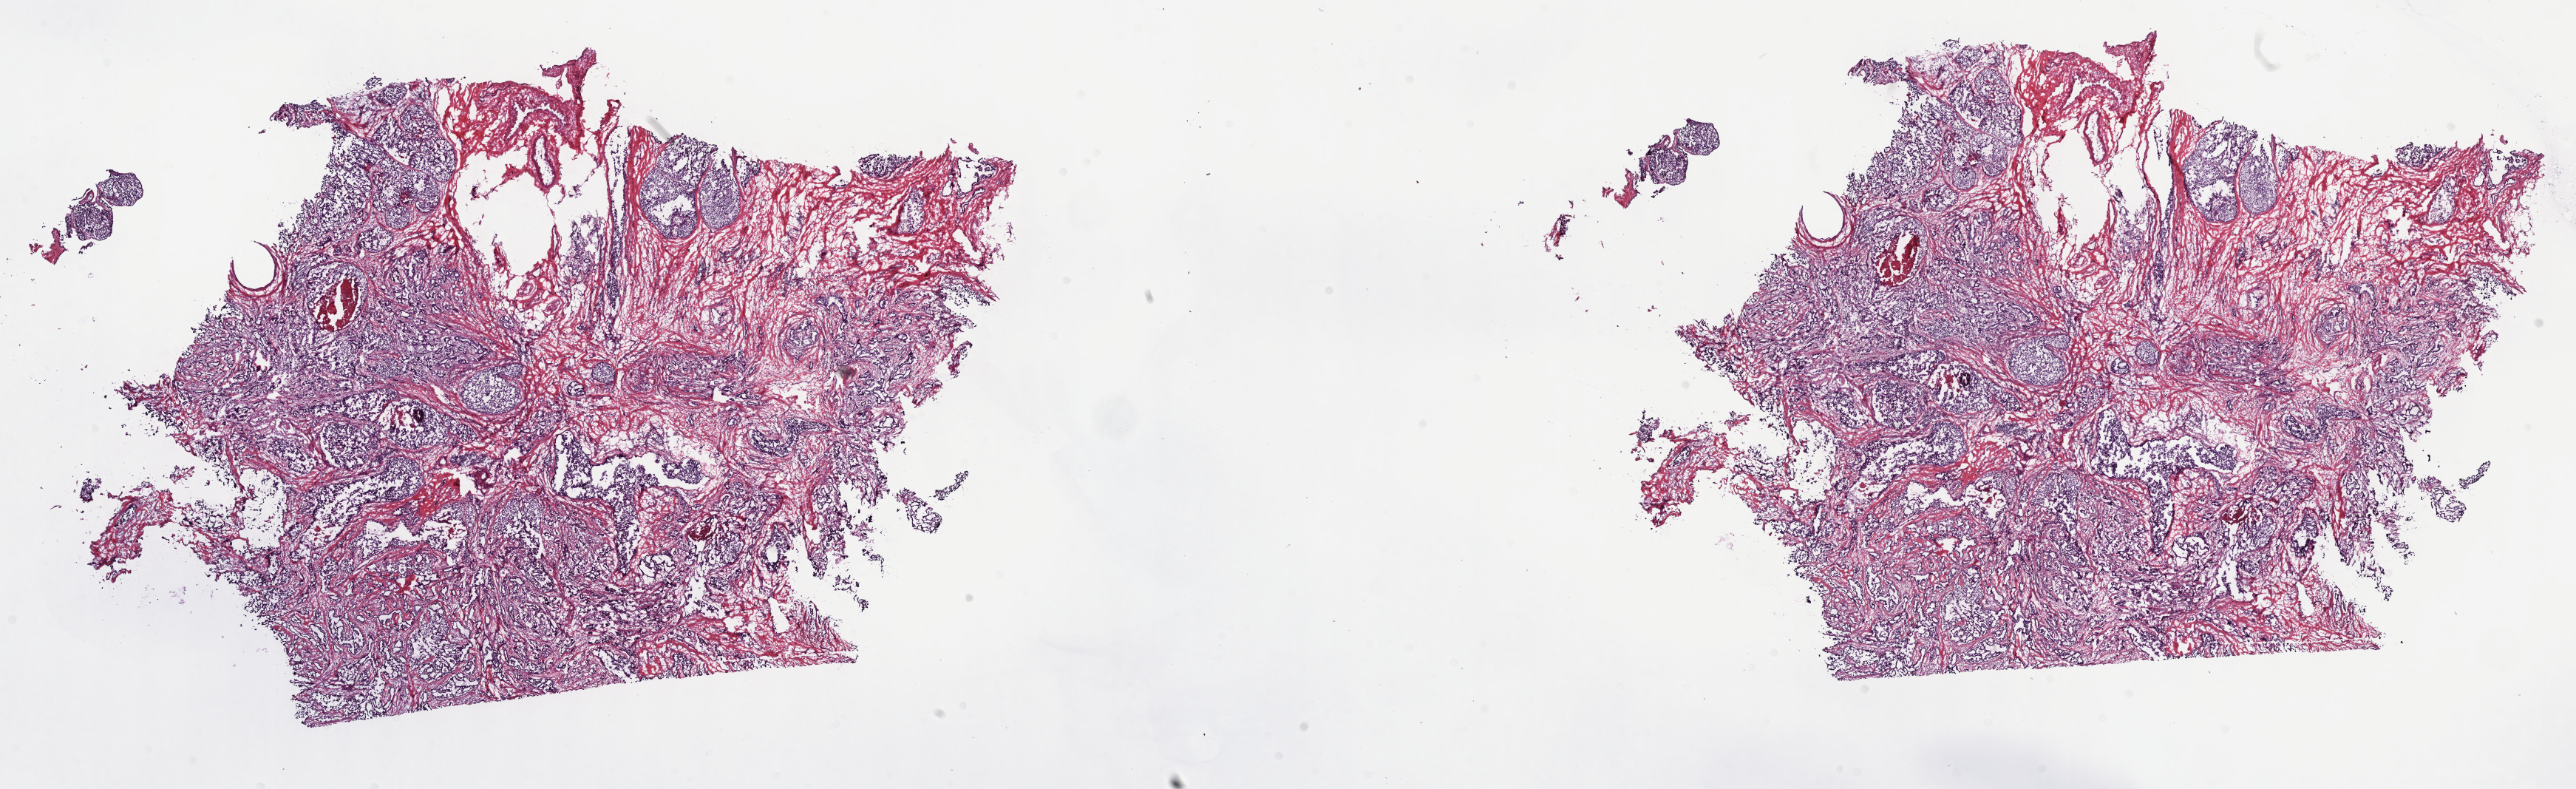
Whole-slide histology image, Hematoxylin and eosin (H&E) stained, a low-resolution overview of the entire scanned area, about 28.2 x 8.6 mm (from a 40x scan). Frozen section from the top of the tissue portion. Primary tumour sample from the breast. Patient: female, age at initial diagnosis 52 years. Pathologist review of this section (percent, as recorded): tumour cells 60%, tumour nuclei 60%, normal cells 5%, stromal cells 30%, necrosis 5%. Inflammatory infiltration, as recorded: lymphocyte infiltration 2%, monocyte infiltration 0%, neutrophil infiltration 0%.
AJCC pathologic stage: IA. Diagnosis: Infiltrating duct carcinoma, NOS.